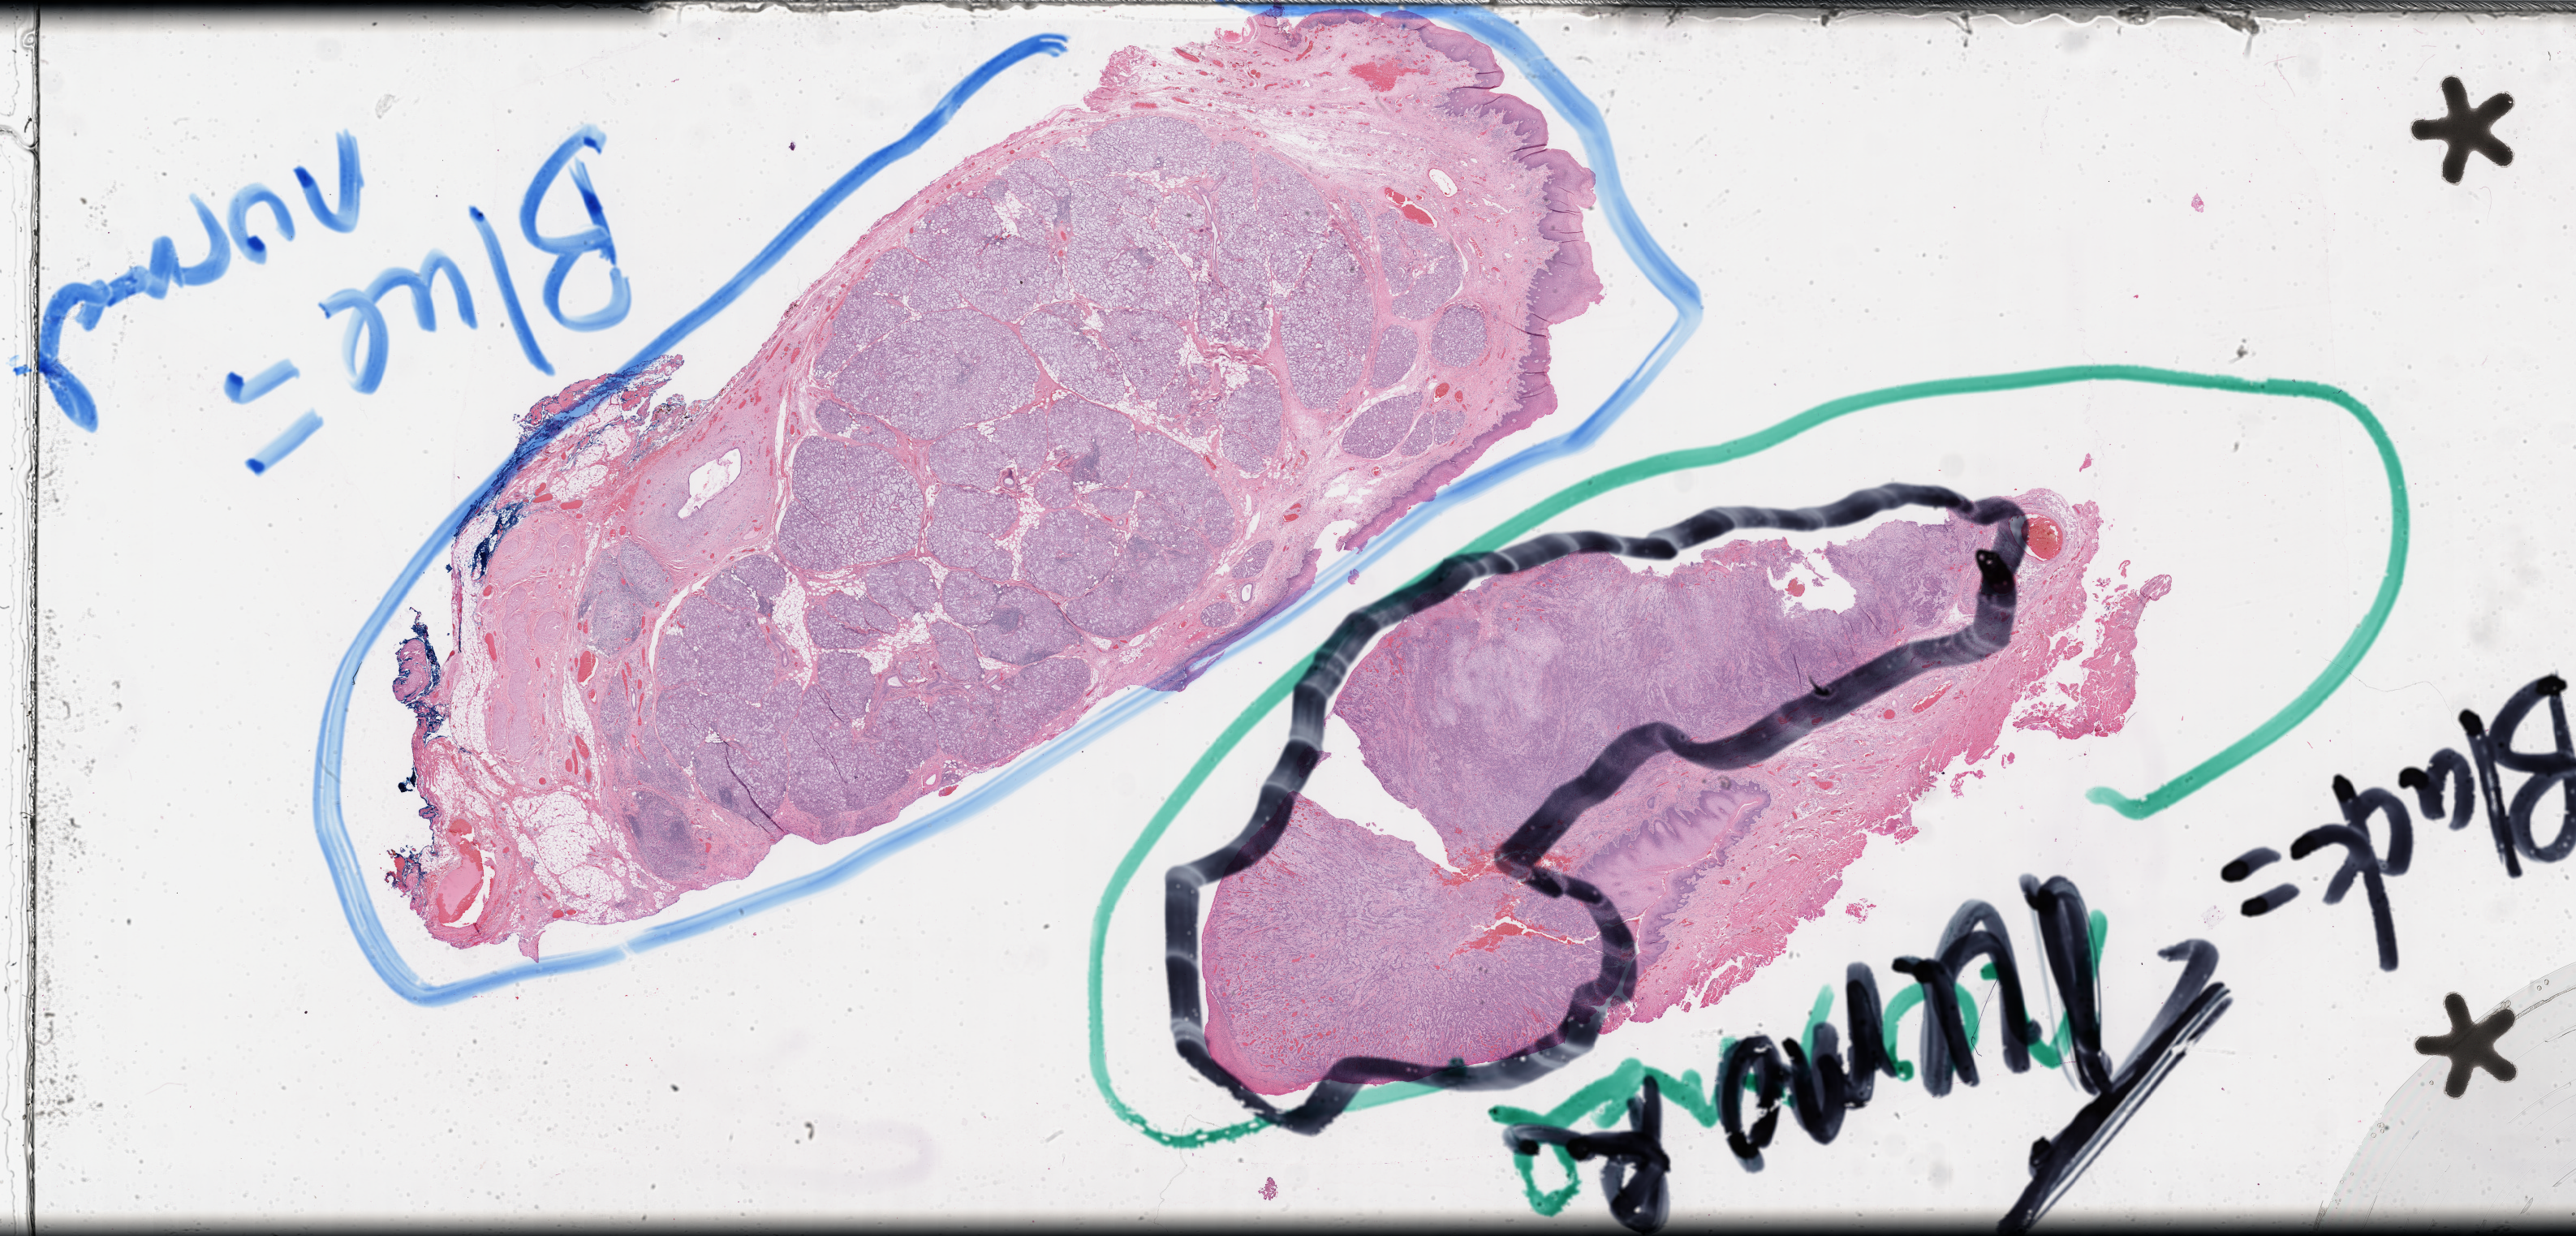
H&E whole-slide image, whole scanned area (about 50.0 x 24.0 mm, slide scanned at 40x) shown as a low-resolution overview. FFPE section. Head and neck, primary tumour sample. Patient: male, age at initial diagnosis 54 years. Histologic grade: G2 (moderately differentiated).
• histologic diagnosis: Squamous cell carcinoma, keratinizing, NOS (floor of mouth, NOS)
• AJCC pathologic stage: IVA (6th edition)
• laterality: left
• TNM: T4a N1 MX